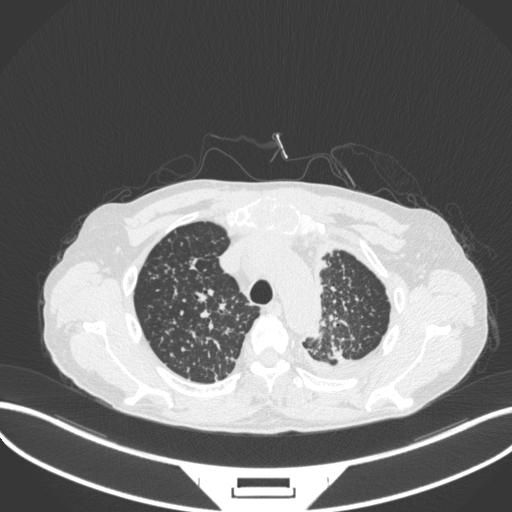
Chest CT, one axial slice. Slice 279 of 319 in the series (ordered by position). Reconstruction kernel B31f. Lung window (W 1500 / L -600 HU). 1 mm slice thickness. 512 × 512 image matrix. Male patient, age 58 years. Case-level facts recorded for this patient, not image findings: clinical TNM (as recorded): T1c N3 M1.
Structures marked on this image (bounding box drawn by a radiologist):
- lung tumour (recorded histology: adenocarcinoma): bounding box (x1, y1, x2, y2) in pixels: (324, 328, 349, 364)